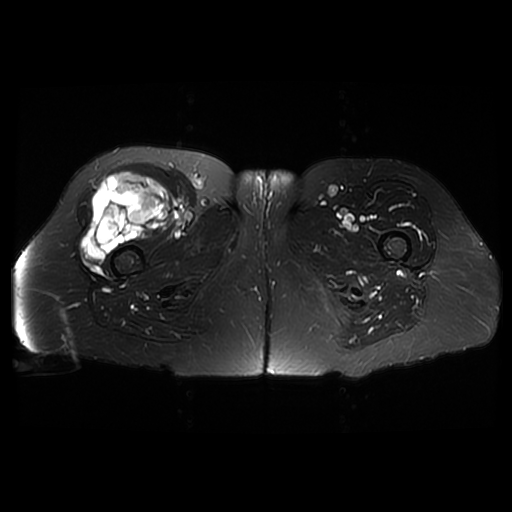
MRI of an extremity soft-tissue mass, one axial slice; slice 29 of 42 in the series (ordered by position); T2-weighted fat-saturated; 6 mm slice thickness; 512 × 512 image matrix, field of view 440 × 440 mm. Female patient. Case-level facts recorded for this patient, not image findings: histological type: pleiomorphic undifferentiated sarcoma; grade: high; site of the primary tumour: right quadricep.
Outlined on this slice (expert manual segmentation):
- gross tumour volume including surrounding oedema: box from (x=81, y=172) to (x=170, y=261) px
- gross tumour volume (mass): (x=81, y=172)–(x=170, y=261)